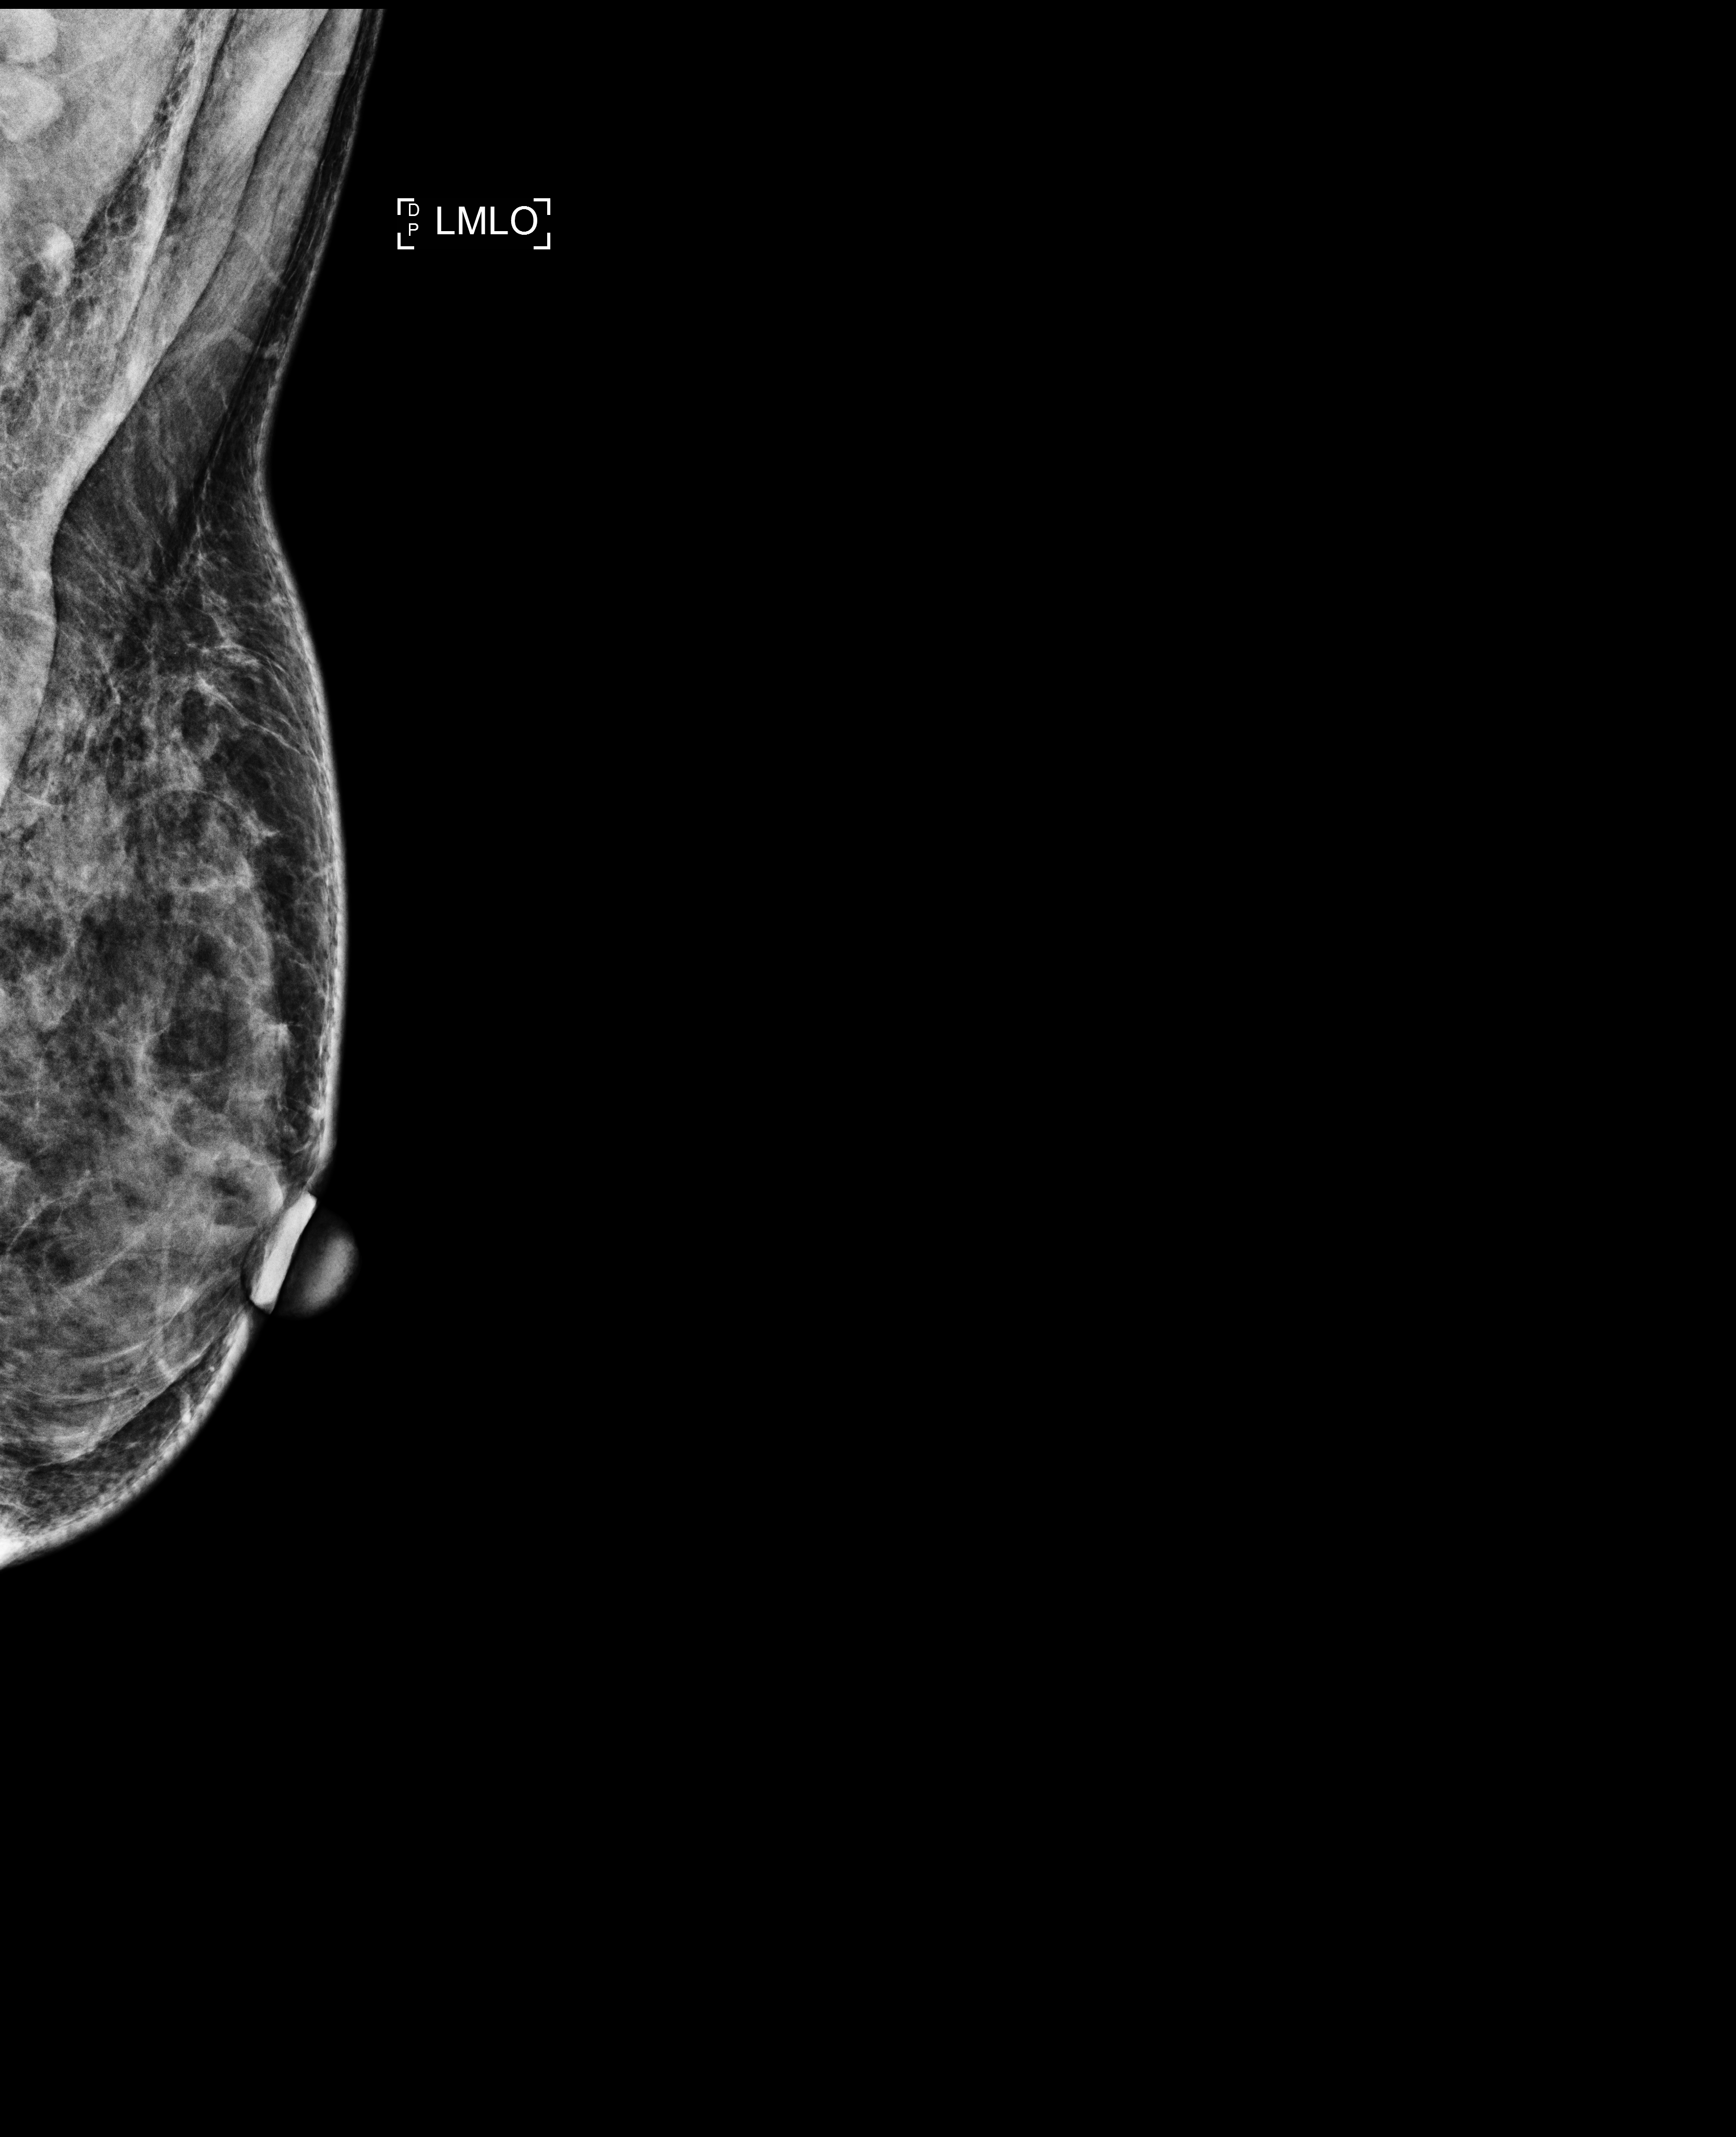
Screening examination, compressed breast thickness 35 mm. Patient aged 60 years (female).
Image type: full-field digital mammogram. Breast: left. Projection: MLO view.